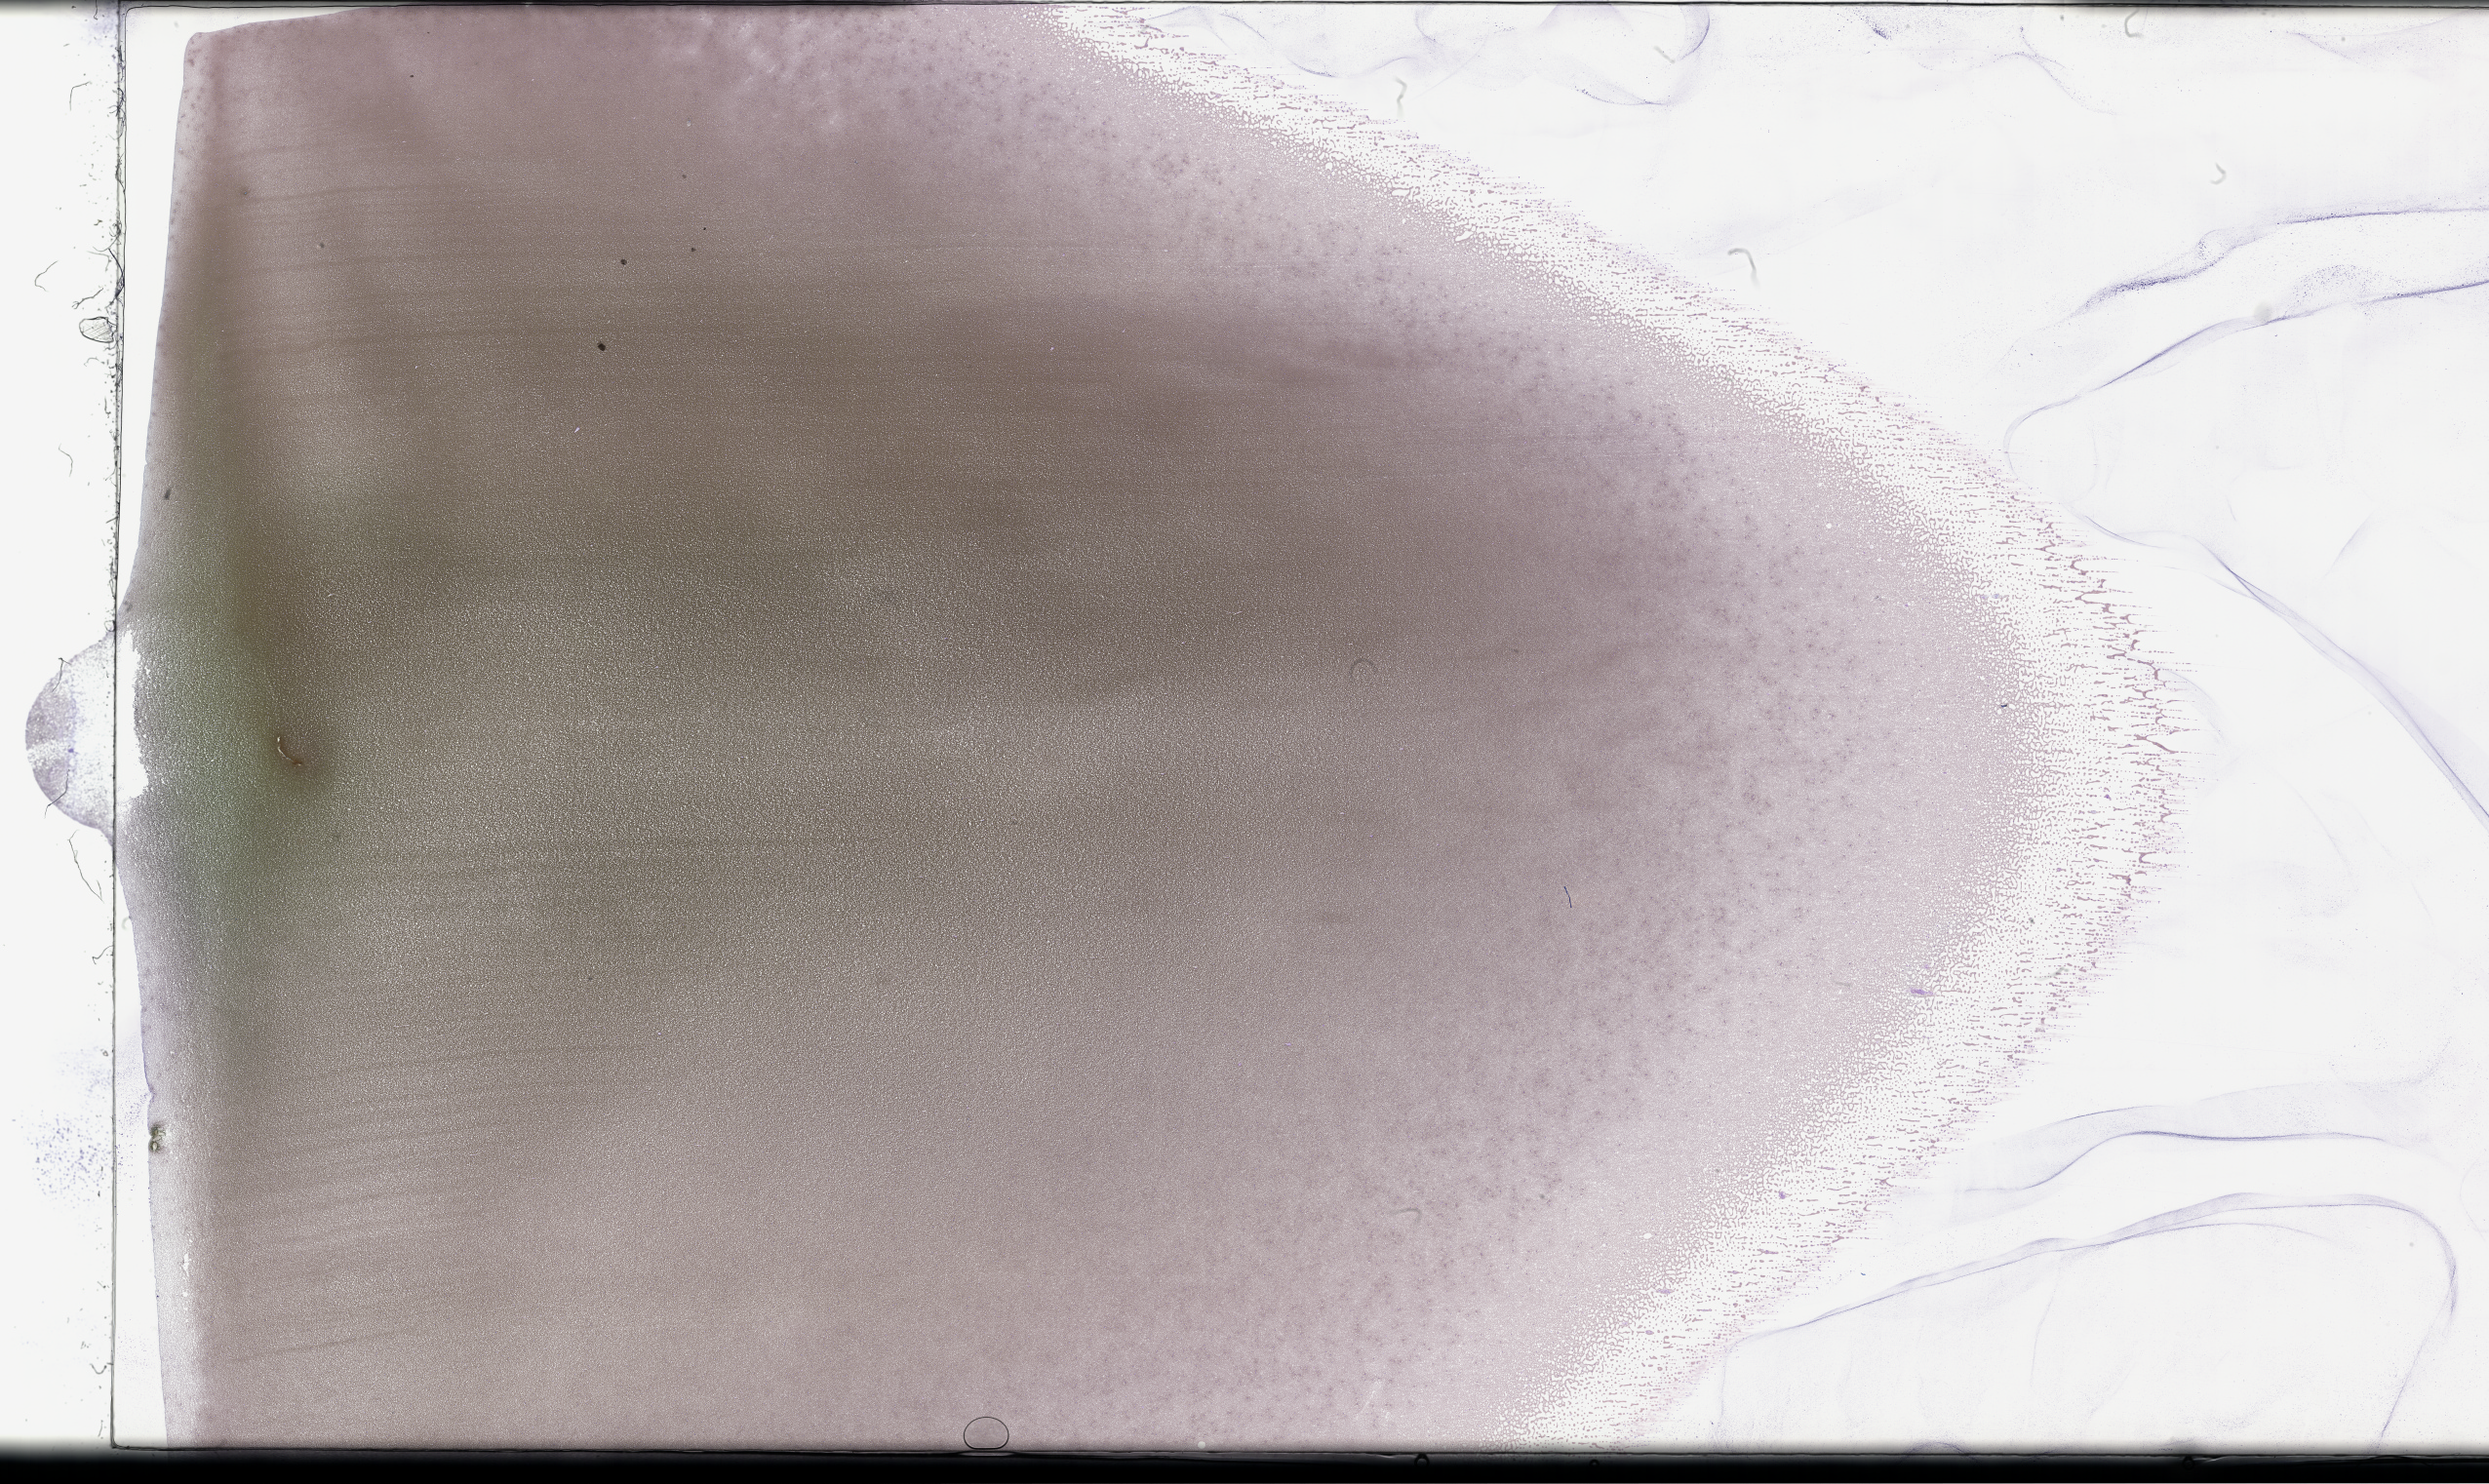
Wright-Giemsa-stained whole blood smear, whole-slide image, shown as a low-resolution overview of the whole scanned area (about 41.2 x 24.6 mm), EDTA-anticoagulated smear, specimen time point: collected on treatment. Patient: male.
- patient diagnosis: Plasma Cell Myeloma